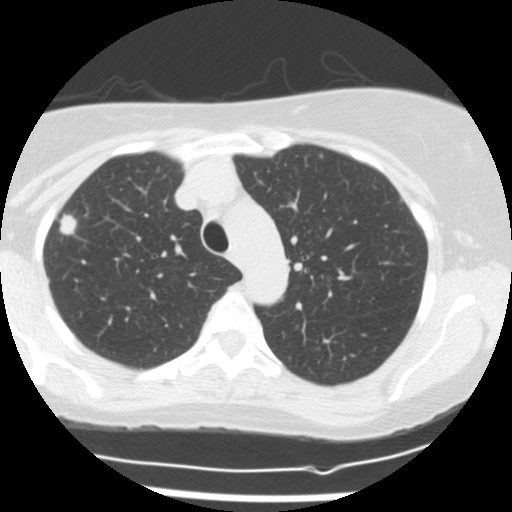
Low-dose screening chest CT, one axial slice. Position 118 of 160 along the scan axis. Reconstruction kernel STANDARD. Lung window (W 1500 / L -600 HU). 2.5 mm slice thickness. 512 × 512 image matrix.
Structures marked on this image (expert manual segmentation):
- lesion 1 (tumor, upper lobe of right lung): bounding box (x1, y1, x2, y2) in pixels: (59, 214, 77, 235)